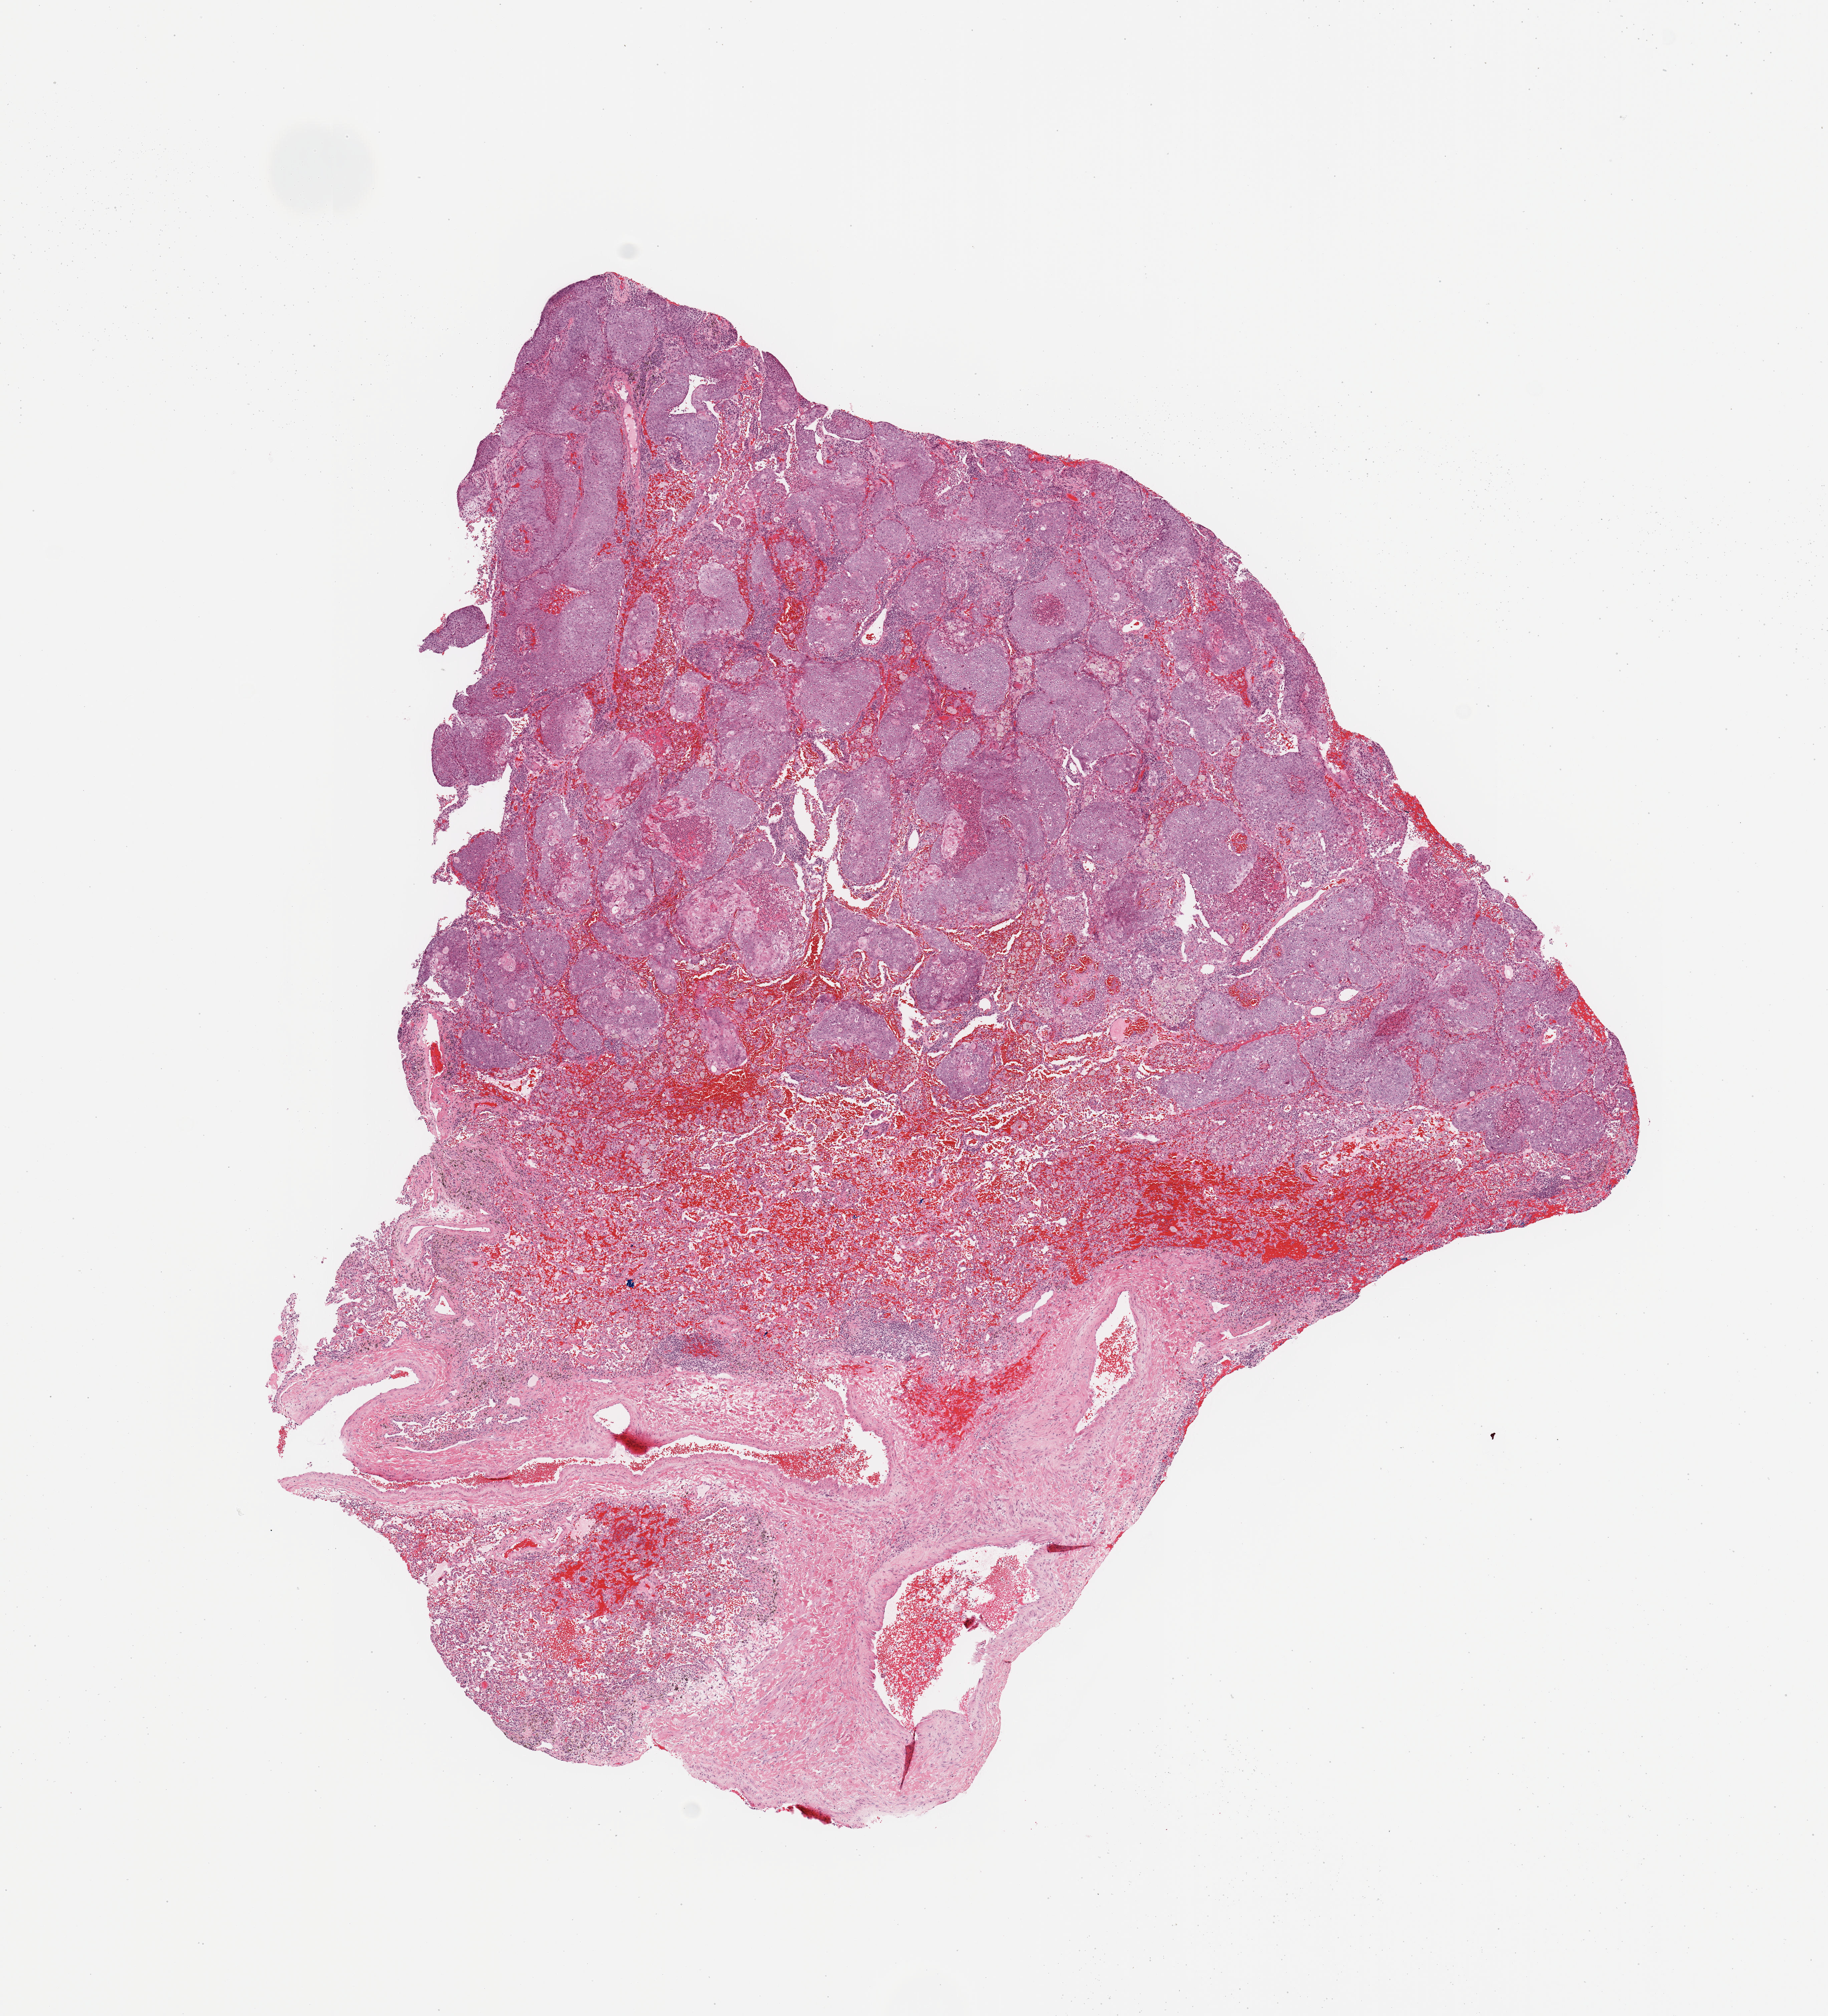
H&E whole-slide image — whole scanned area (about 10.8 x 11.9 mm, slide scanned at 20x) shown as a low-resolution overview. Lung, tumour tissue. 58-year-old male patient.
Histologic diagnosis: Squamous cell carcinoma, NOS.